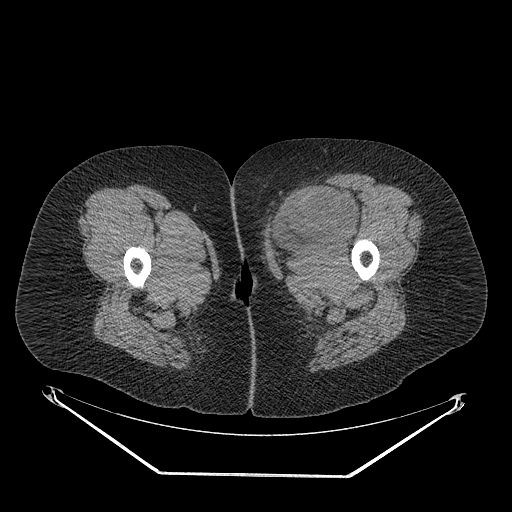
CT of an extremity soft-tissue mass (from a PET/CT study), one axial slice. Slice 33 of 267 in the series (ordered by position). 140 kVp. Soft-tissue window (W 400 / L 40 HU). 512 × 512 image matrix, field of view 500 × 500 mm. Female patient. Case-level facts recorded for this patient, not image findings: histological type: myxofibrosarcoma; grade: intermediate; site of the primary tumour: left thigh.
Outlined on this slice (expert contour drawn on MRI and transferred to this co-registered scan by the dataset authors):
- gross tumour volume including surrounding oedema: box from (x=267, y=185) to (x=359, y=263) px
- gross tumour volume (mass): (x=269, y=185)–(x=355, y=245)